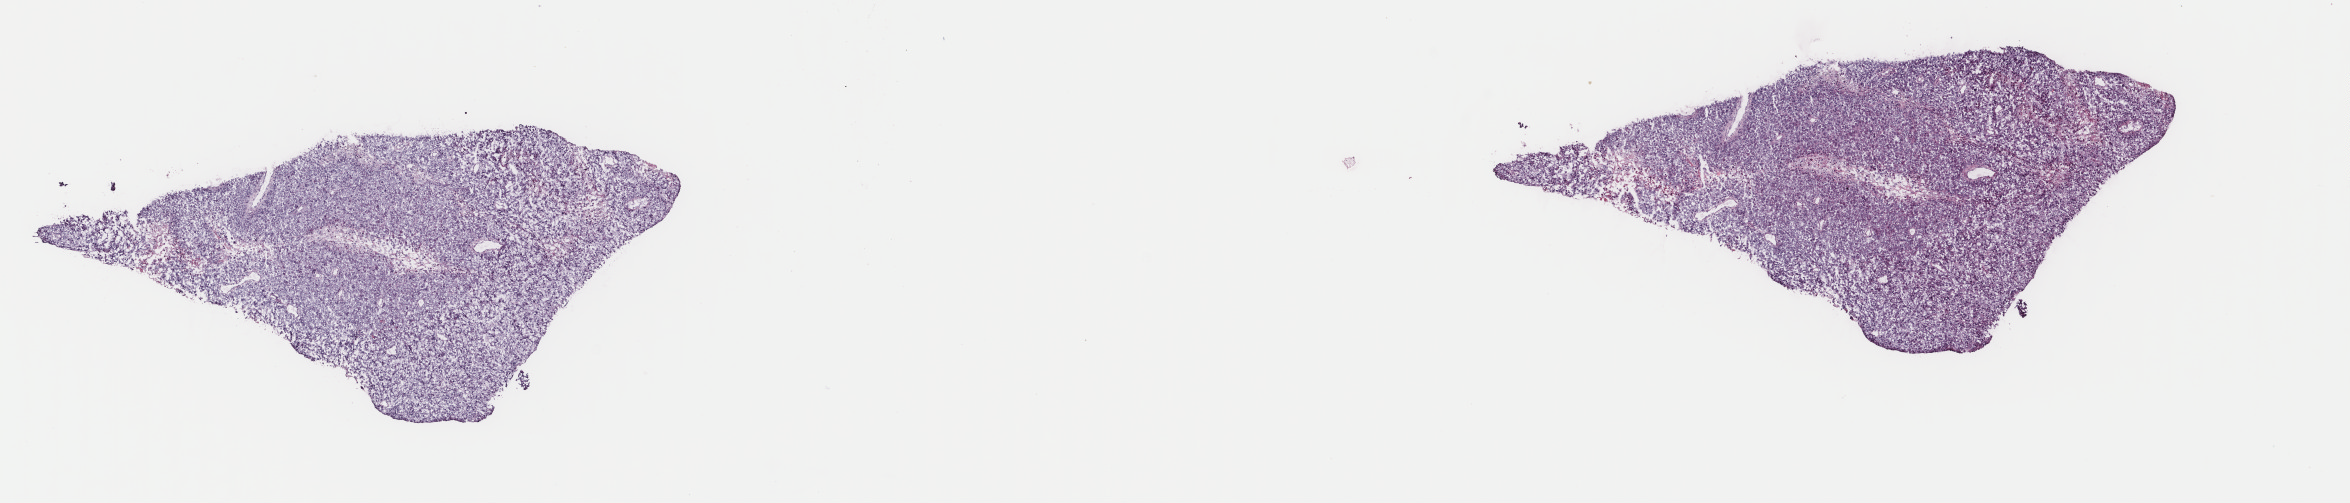
Hematoxylin and eosin (H&E) stained whole-slide image, a low-resolution overview of the entire scanned area, about 18.7 x 4.0 mm. Frozen section from the top of the tissue portion. Metastatic tumour sample, sampled site not recorded. Male patient; age at initial diagnosis 70 years. Composition of this section per pathologist review: tumour cells 84%, tumour nuclei 97%, normal cells 1%, stromal cells 0%, necrosis 15%. Infiltration values recorded for this section: lymphocyte infiltration 1%, monocyte infiltration 1%, neutrophil infiltration 0%.
This section: metastatic tumour tissue. Patient diagnosis: Malignant melanoma, NOS.